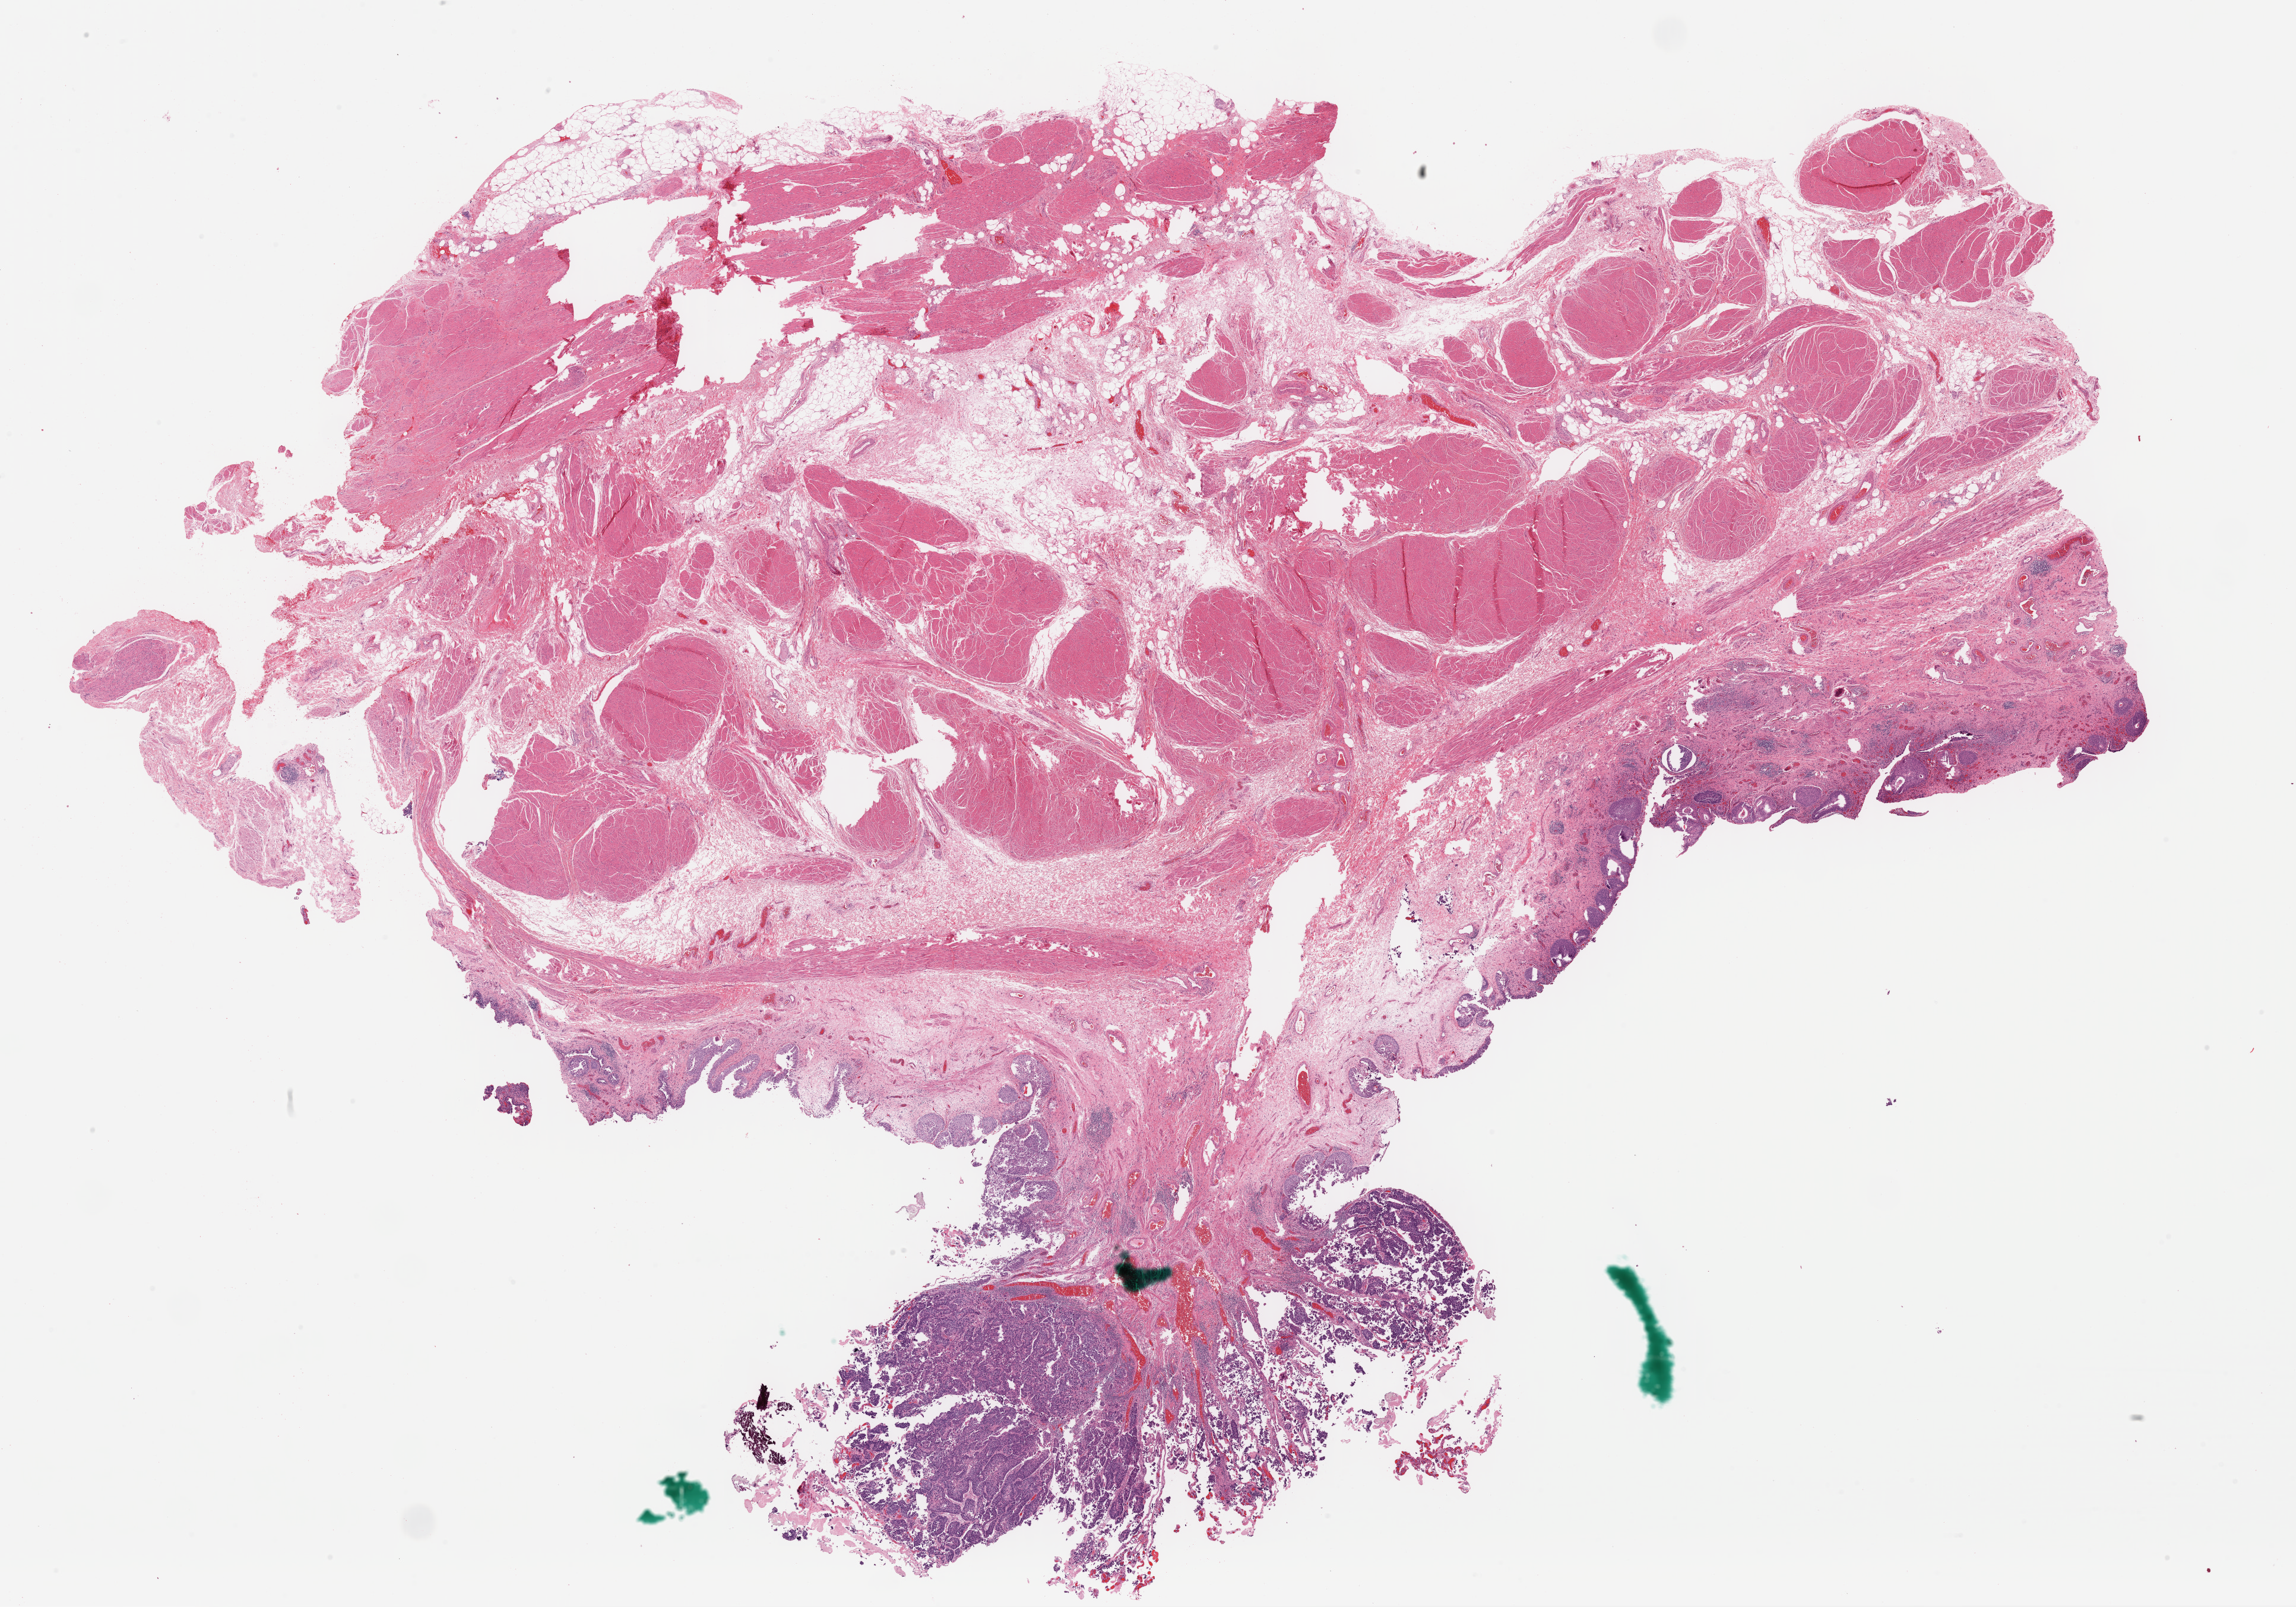
Whole-slide histology image, Hematoxylin and eosin (H&E) stained, a low-resolution overview of the entire scanned area, about 30.5 x 21.4 mm (slide scanned at 40x), formalin-fixed paraffin-embedded (FFPE) diagnostic section, sample: primary tumour, bladder. Male patient; age at initial diagnosis 71 years. Histologic grade: high grade.
• AJCC pathologic stage: II (6th edition)
• pathologic diagnosis: Transitional cell carcinoma
• TNM: T2b N0 M0